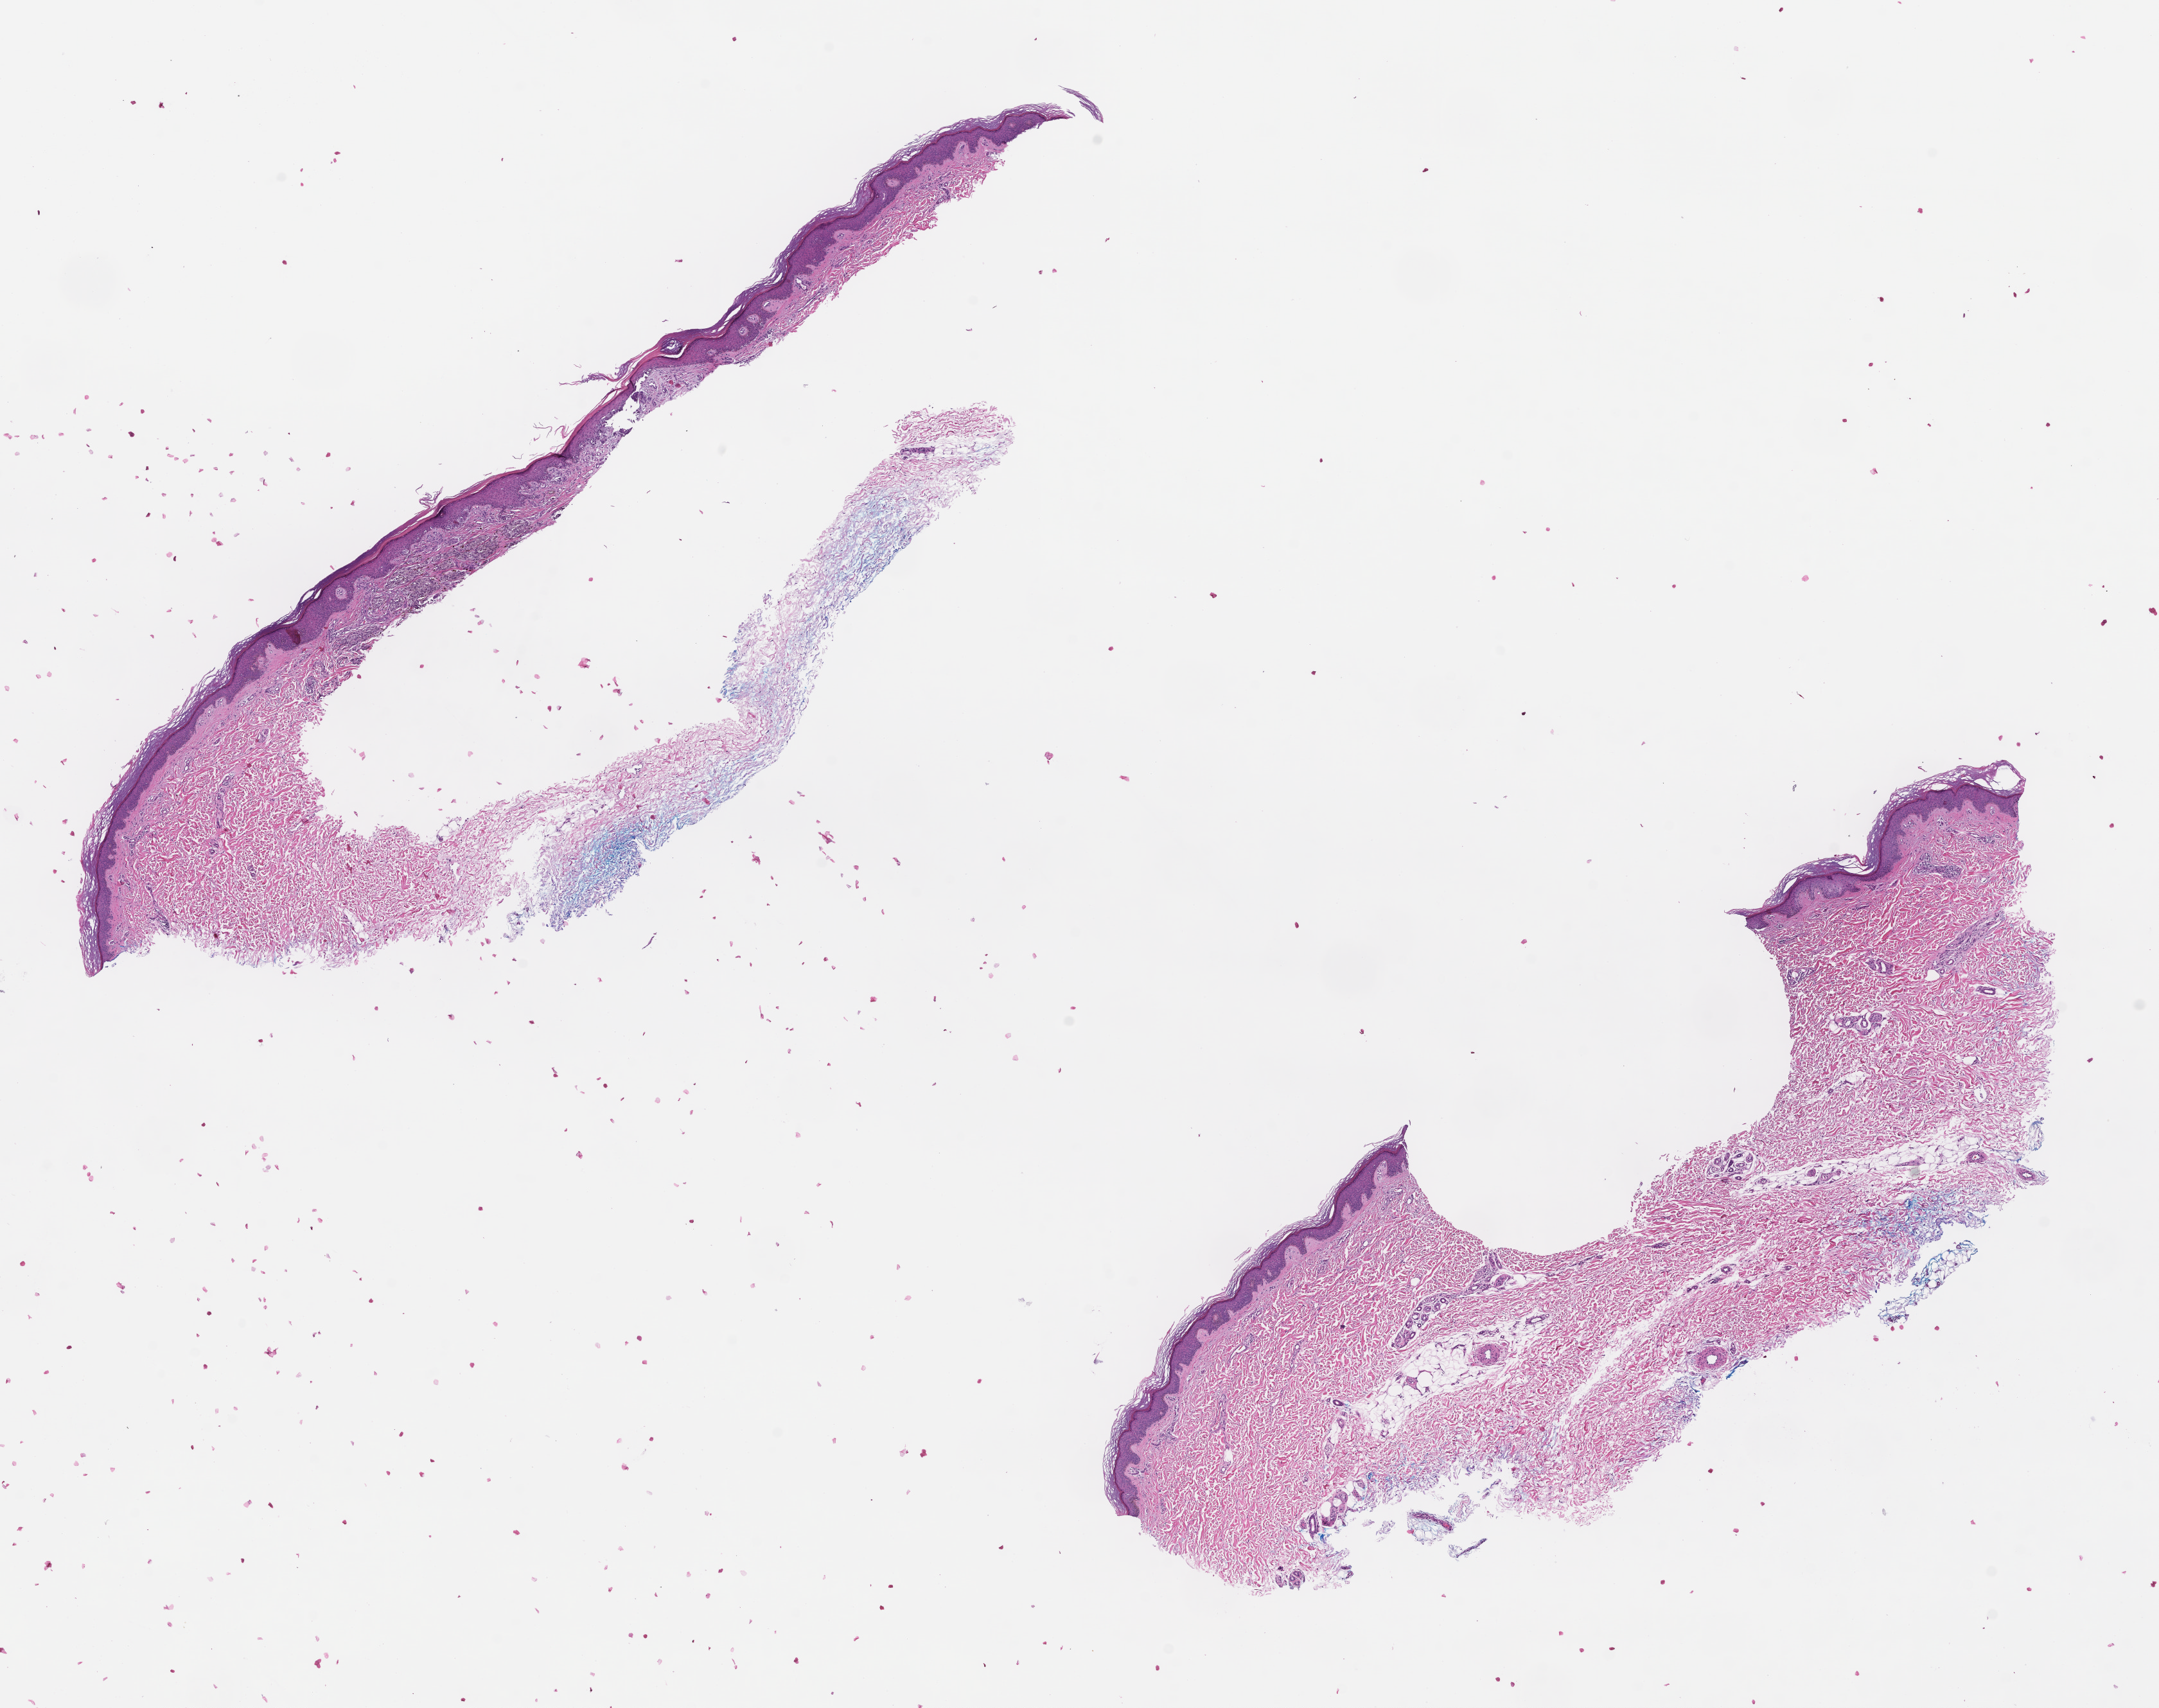
Haematoxylin and eosin whole-slide image — whole scanned area (about 13.6 x 10.7 mm) shown as a low-resolution overview. FFPE section. Site: skin. Patient: female.
This section: primary tumour tissue. Diagnosis: Melanoma.